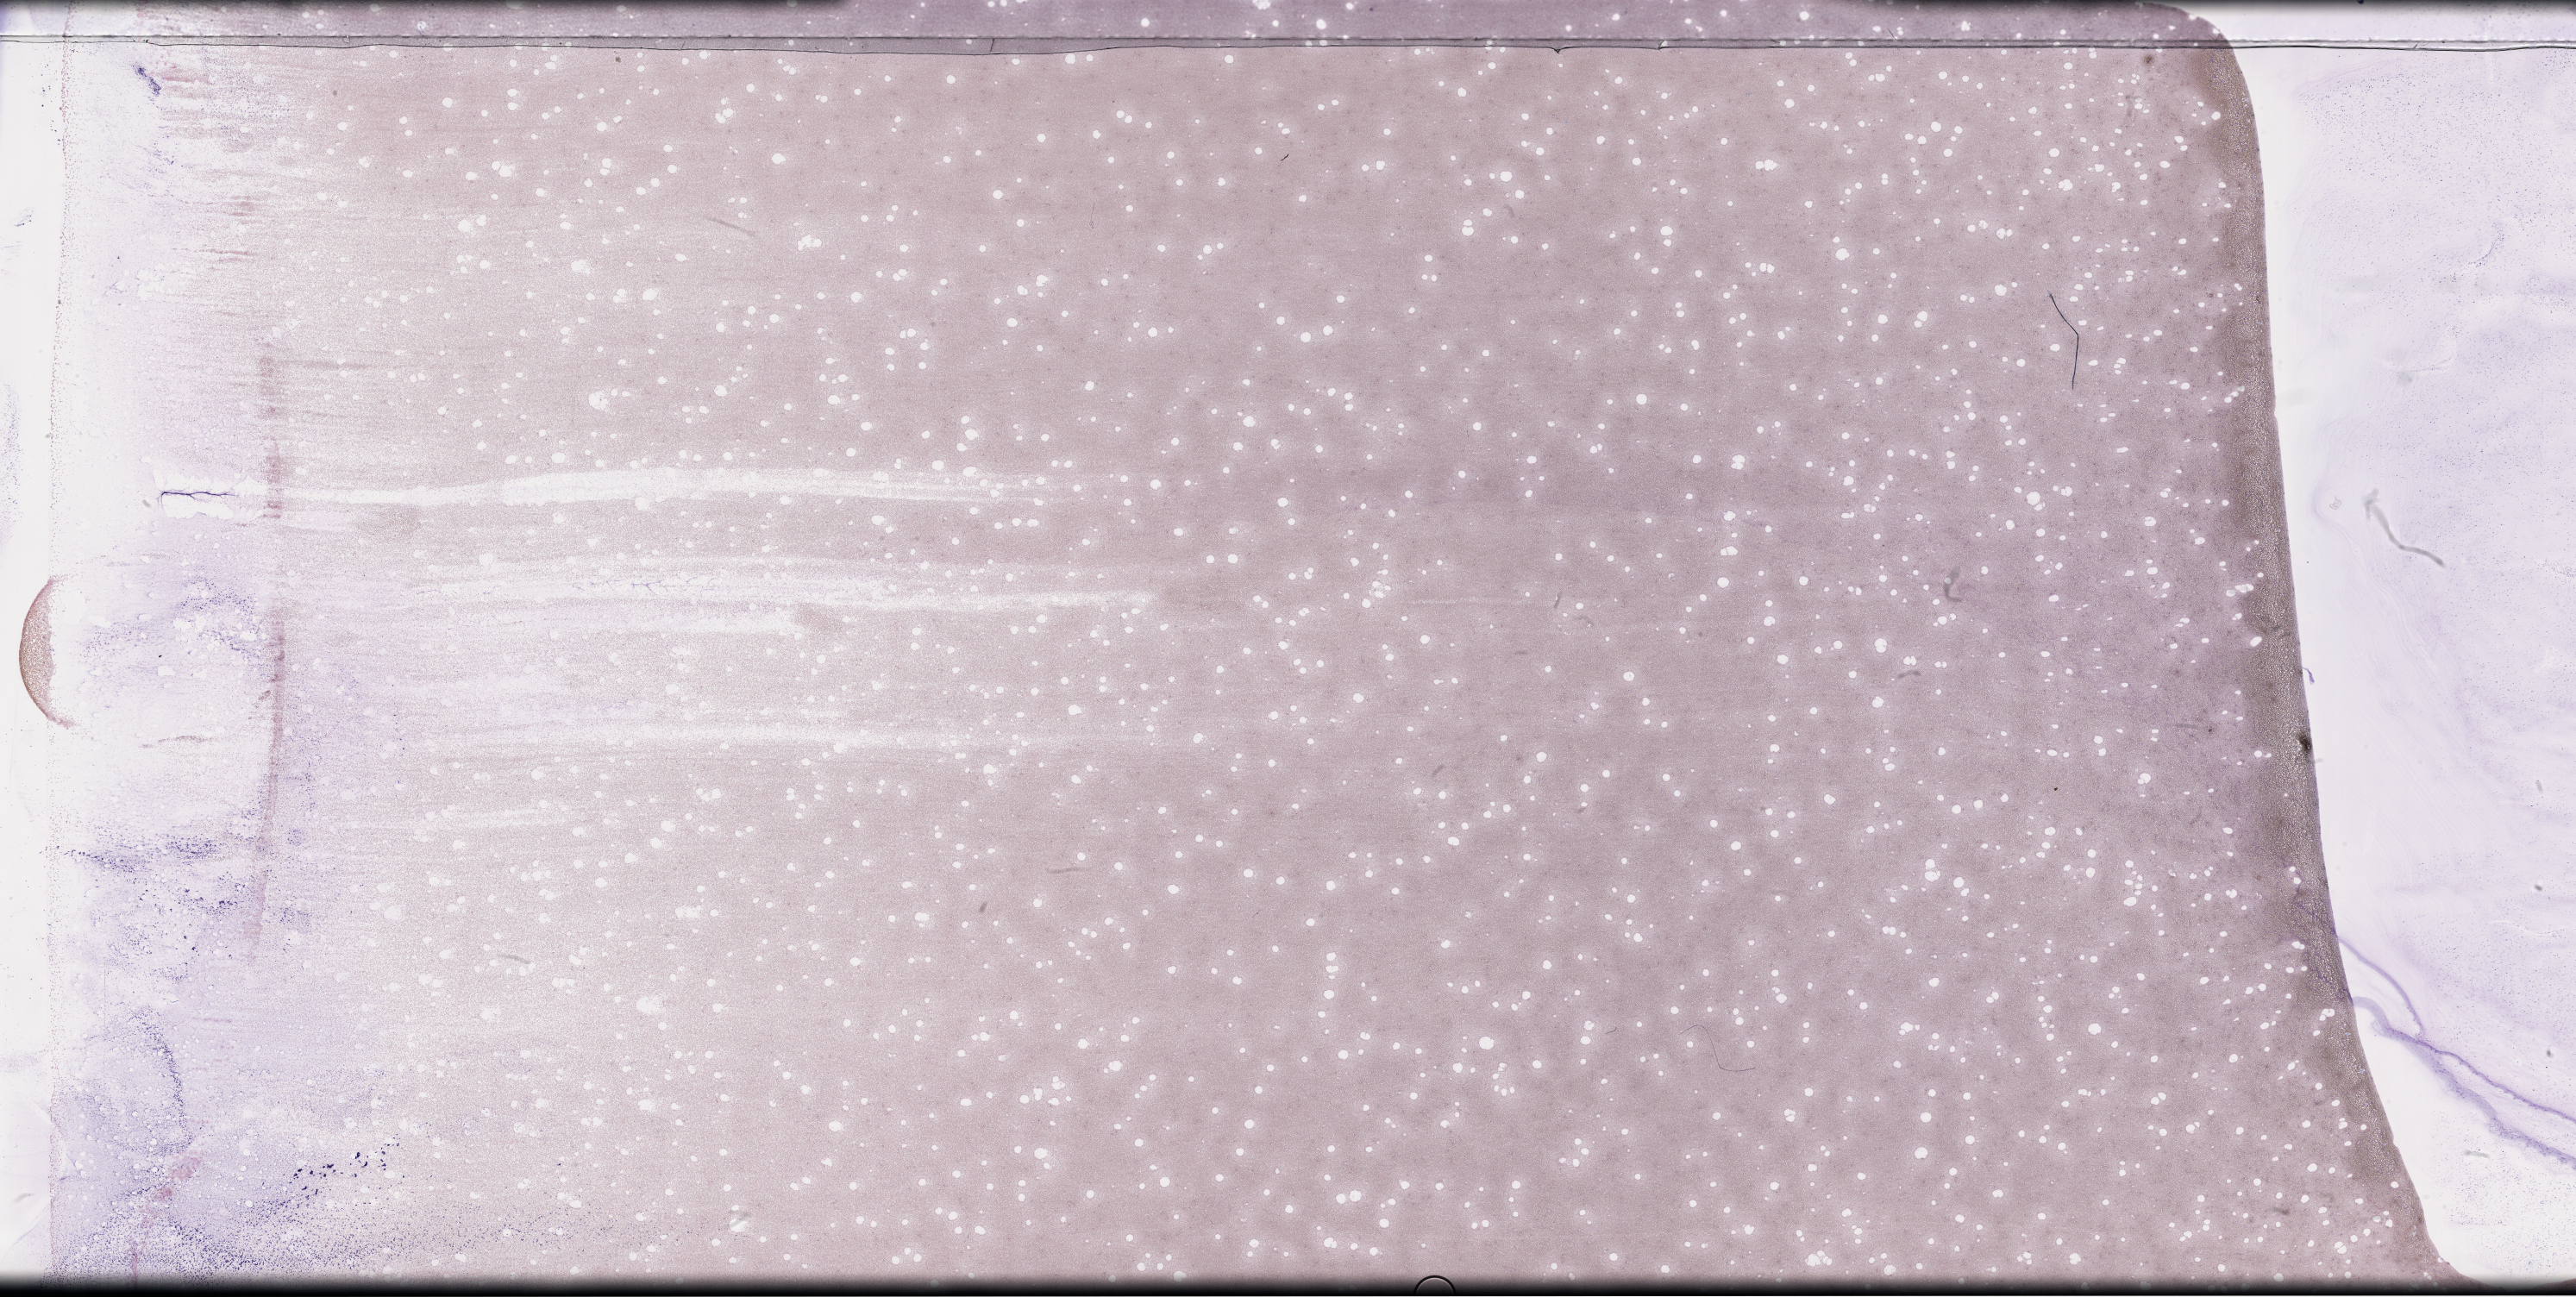
Whole-slide image of a whole blood smear, Wright–Giemsa stain, whole scanned area (about 48.2 x 24.3 mm) shown as a low-resolution overview, specimen time point: collected at disease progression. Patient: female.
• from a patient with: Plasma Cell Myeloma